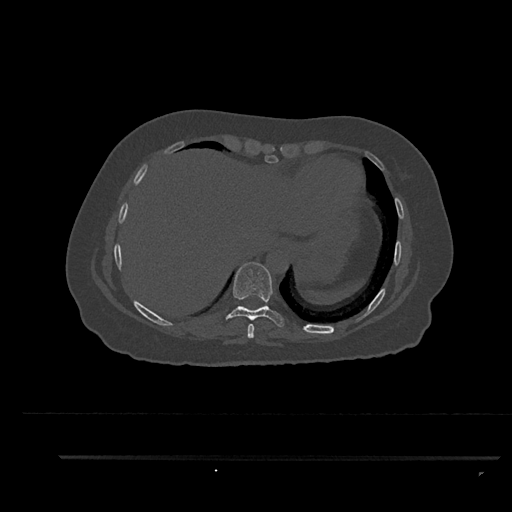
CT including the spine, one axial slice; slice 416 of 797 in the series (ordered by position); 120 kVp; bone window (W 1800 / L 400 HU); 512 × 512 image matrix. Female patient, age 44 years. From the clinical record (not read from this slice): primary cancer: renal; vertebrae with lytic lesions (as recorded): L1.
Structures marked on this image (semi-automatic segmentation, software-assisted and operator-edited):
- T8 vertebra: box from (x=247, y=324) to (x=255, y=339) px
- T9 vertebra: (x=226, y=262)–(x=284, y=327)